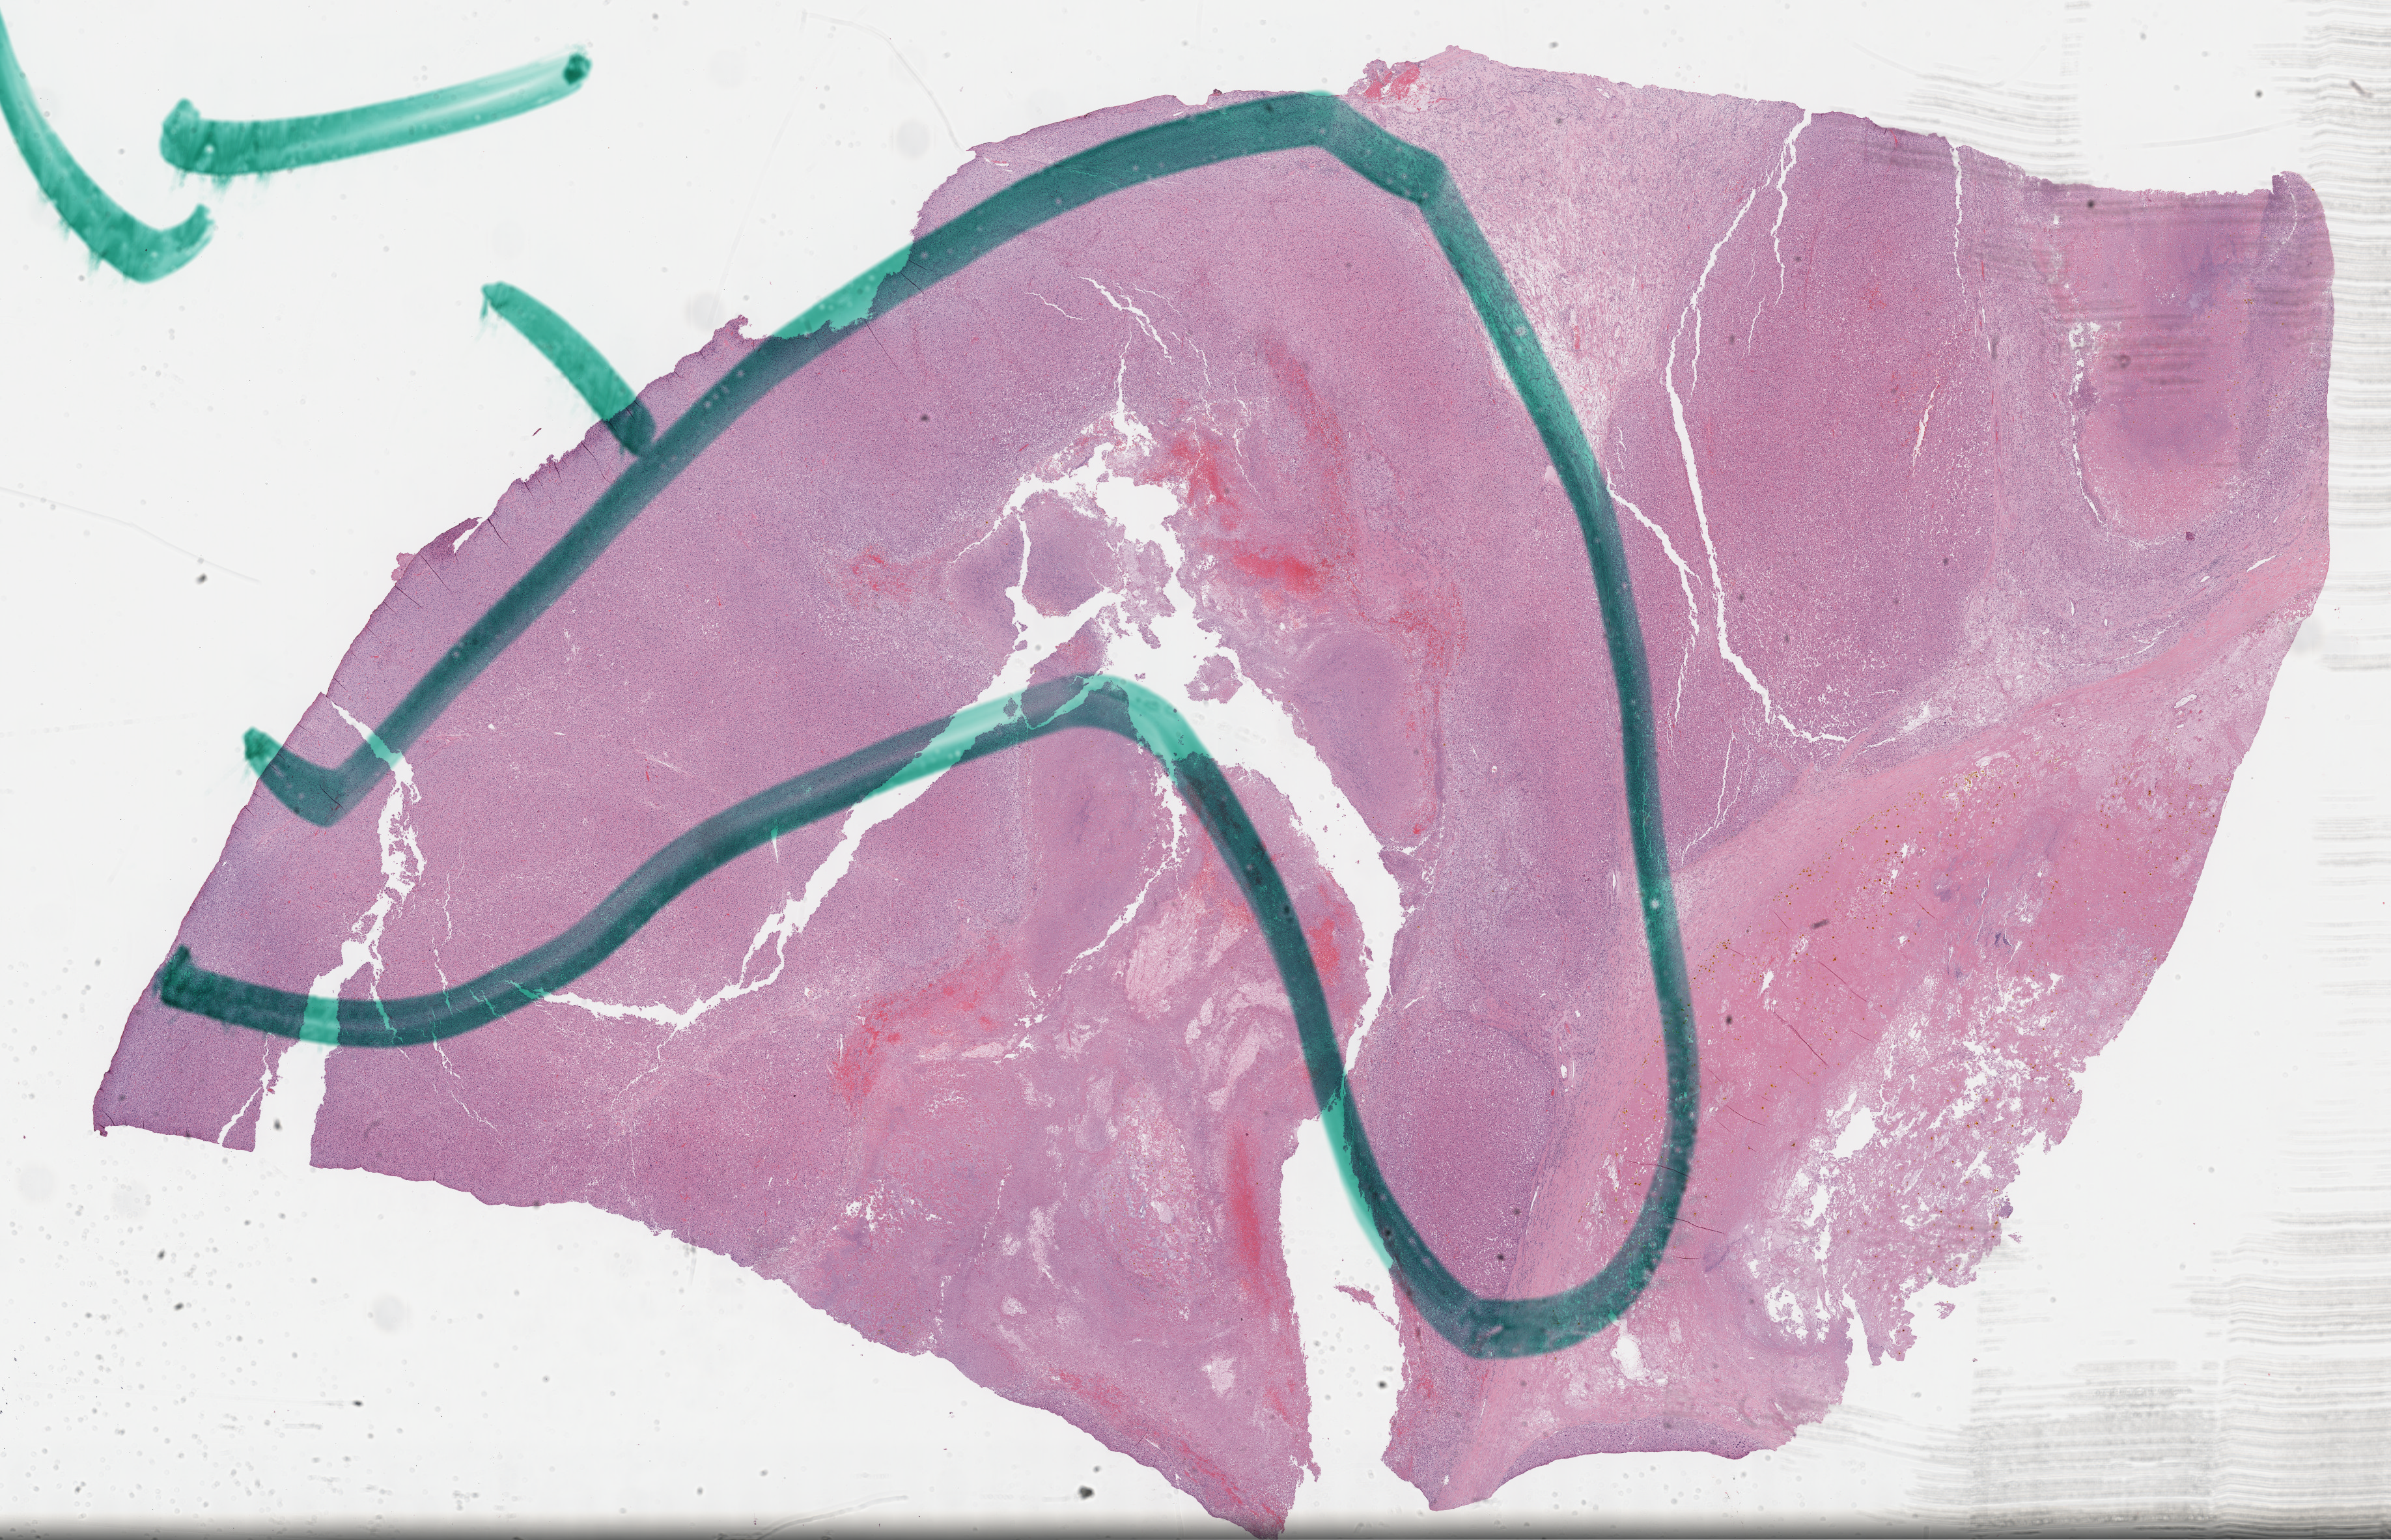
Digitized H&E-stained tissue section (whole slide) — a low-resolution overview of the entire scanned area, about 29.7 x 19.1 mm (from a 40x scan). Formalin-fixed paraffin-embedded (FFPE) diagnostic section. Primary tumour sample from the adrenal cortex. Female, age 65 years at initial diagnosis.
* histologic diagnosis: Adrenal cortical carcinoma (cortex of adrenal gland)
* lymph nodes positive (case pathology): 0 of 17 examined
* laterality: left